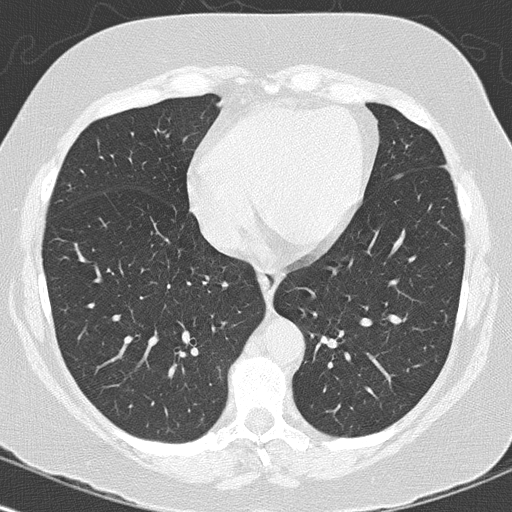
Low-dose screening chest CT, one axial slice. Slice 53 of 144 in the series (ordered by position). Reconstruction kernel B50f. 120 kVp. Lung window (W 1500 / L -600 HU). 2 mm slice thickness. 512 × 512 image matrix.
Annotated regions visible in this slice (manually delineated by an expert):
- lesion 1 (tumor, lower lobe of left lung): bounding box <363,306,368,310> (left, top, right, bottom; pixels)